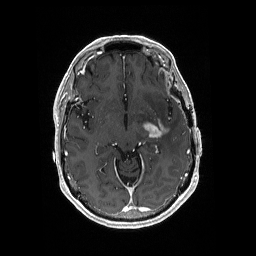
Brain MRI from a brain-tumour surgery series, one axial slice. Slice 108 of 176 in the series (ordered by position). T1-weighted post-contrast. 256 × 256 image matrix, field of view 256 × 256 mm. Case-level facts recorded for this patient, not image findings: histopathology: Glioblastoma; WHO grade: 4; IDH mutation: no; tumour location: Left Medial Temporal.
Outlined on this slice (expert manual segmentation):
- tumour: bounding box (x1, y1, x2, y2) in pixels: (142, 118, 170, 140)